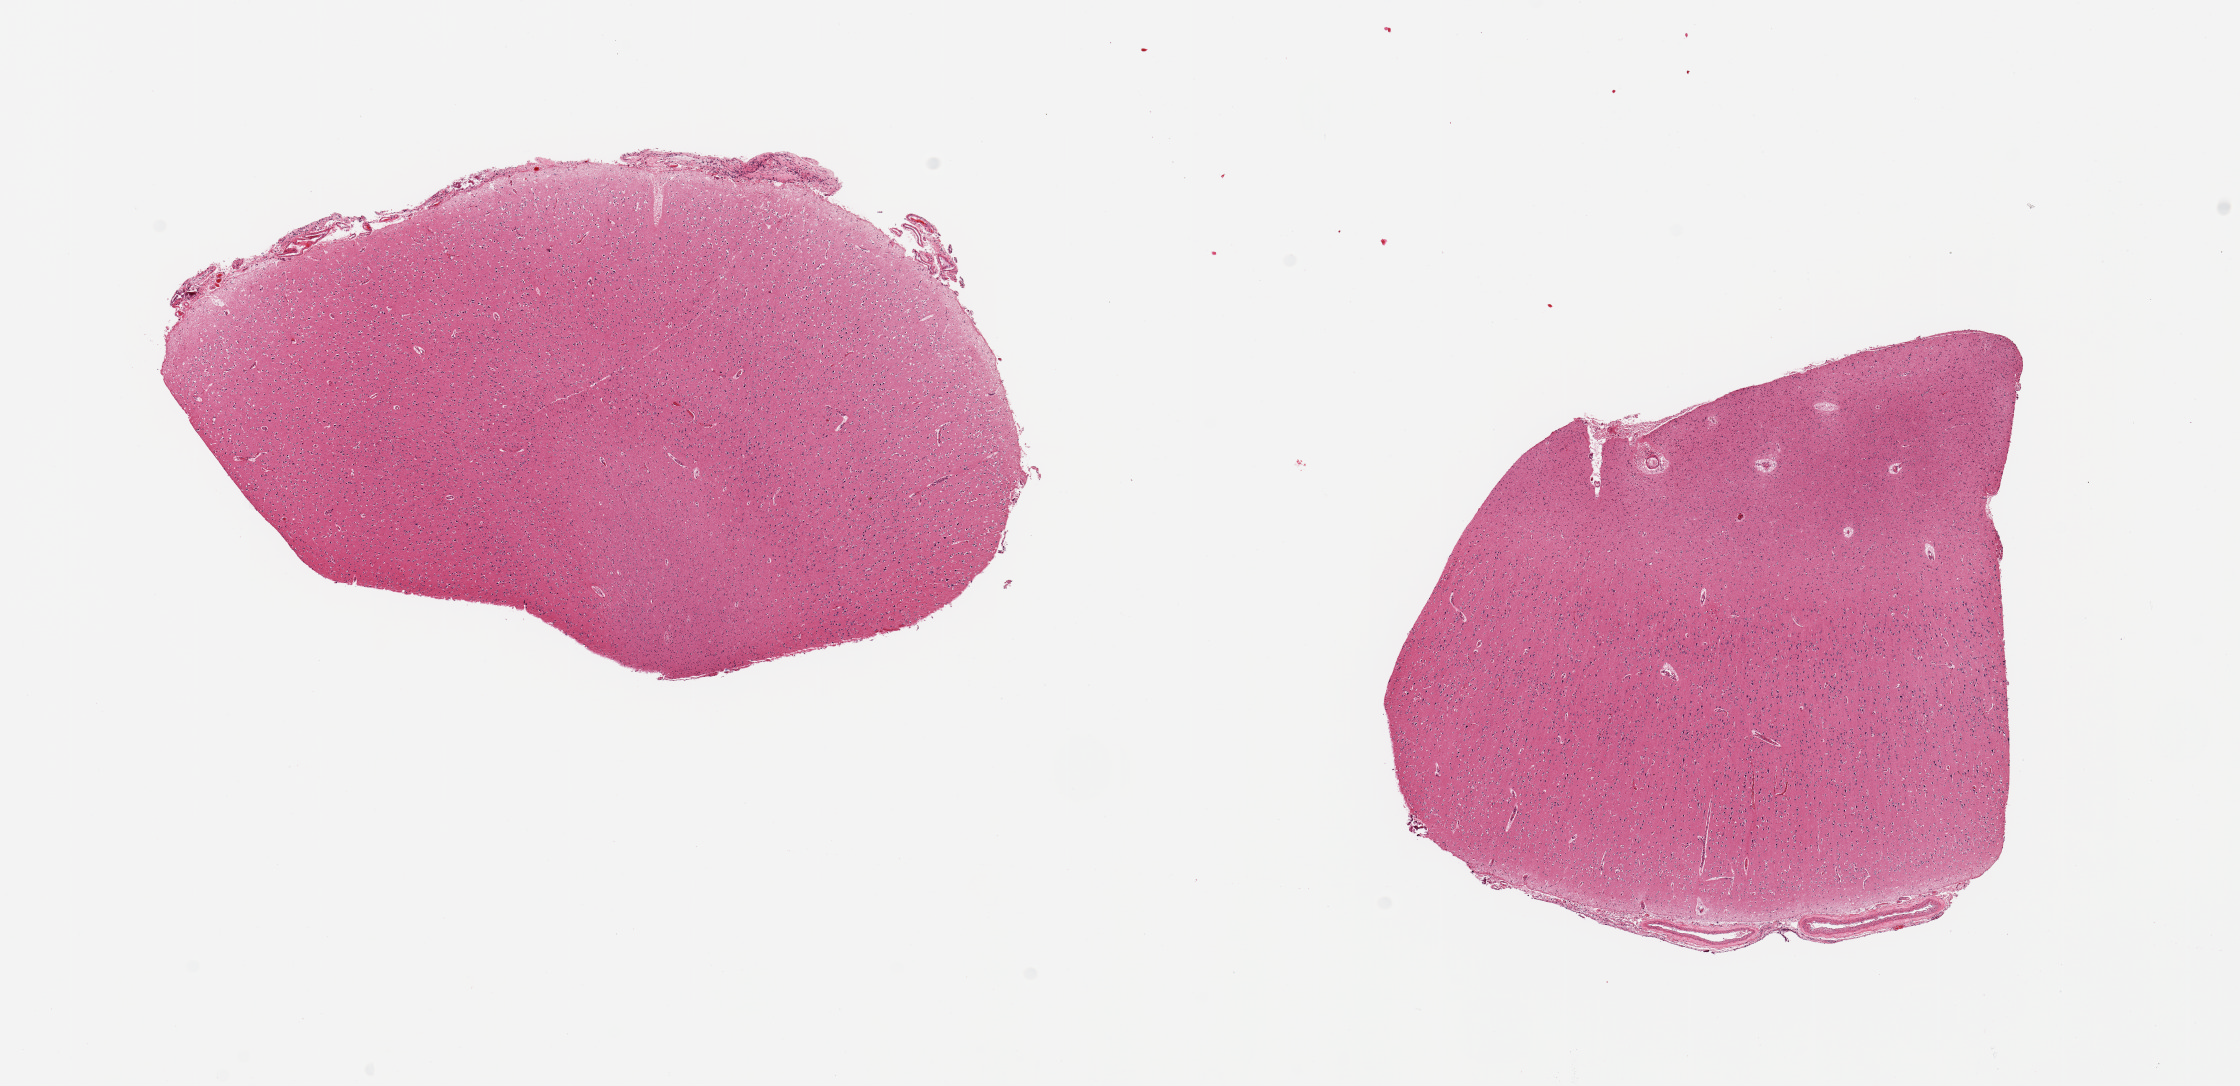
Digitized H&E-stained section — a low-resolution overview of the entire scanned area, about 17.7 x 8.6 mm (acquisition: 20x scan), PAXgene-fixed paraffin-embedded (PFPE) section, section of cerebral cortex (target tissue), donor tissue sample. Donor: male.
• review note (as recorded): 2 pieces